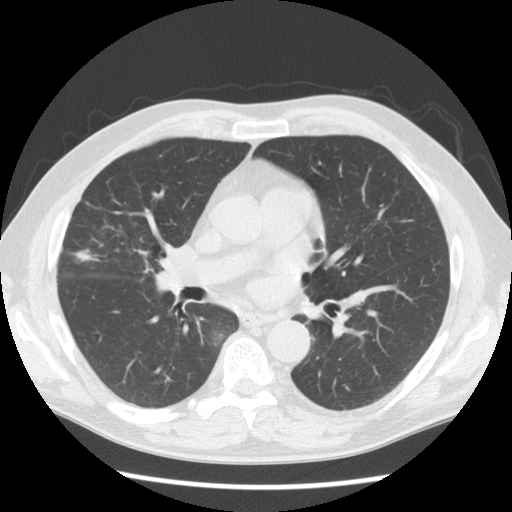
Low-dose screening chest CT, one axial slice; slice 81 of 146 in the series (ordered by position); reconstruction kernel STANDARD; lung window (W 1500 / L -600 HU); 2.5 mm slice thickness; 512 × 512 image matrix, field of view 350 × 350 mm.
Outlined on this slice (manually delineated by an expert):
- lesion 1 (tumor, middle lobe of right lung): box from (x=72, y=250) to (x=101, y=262) px